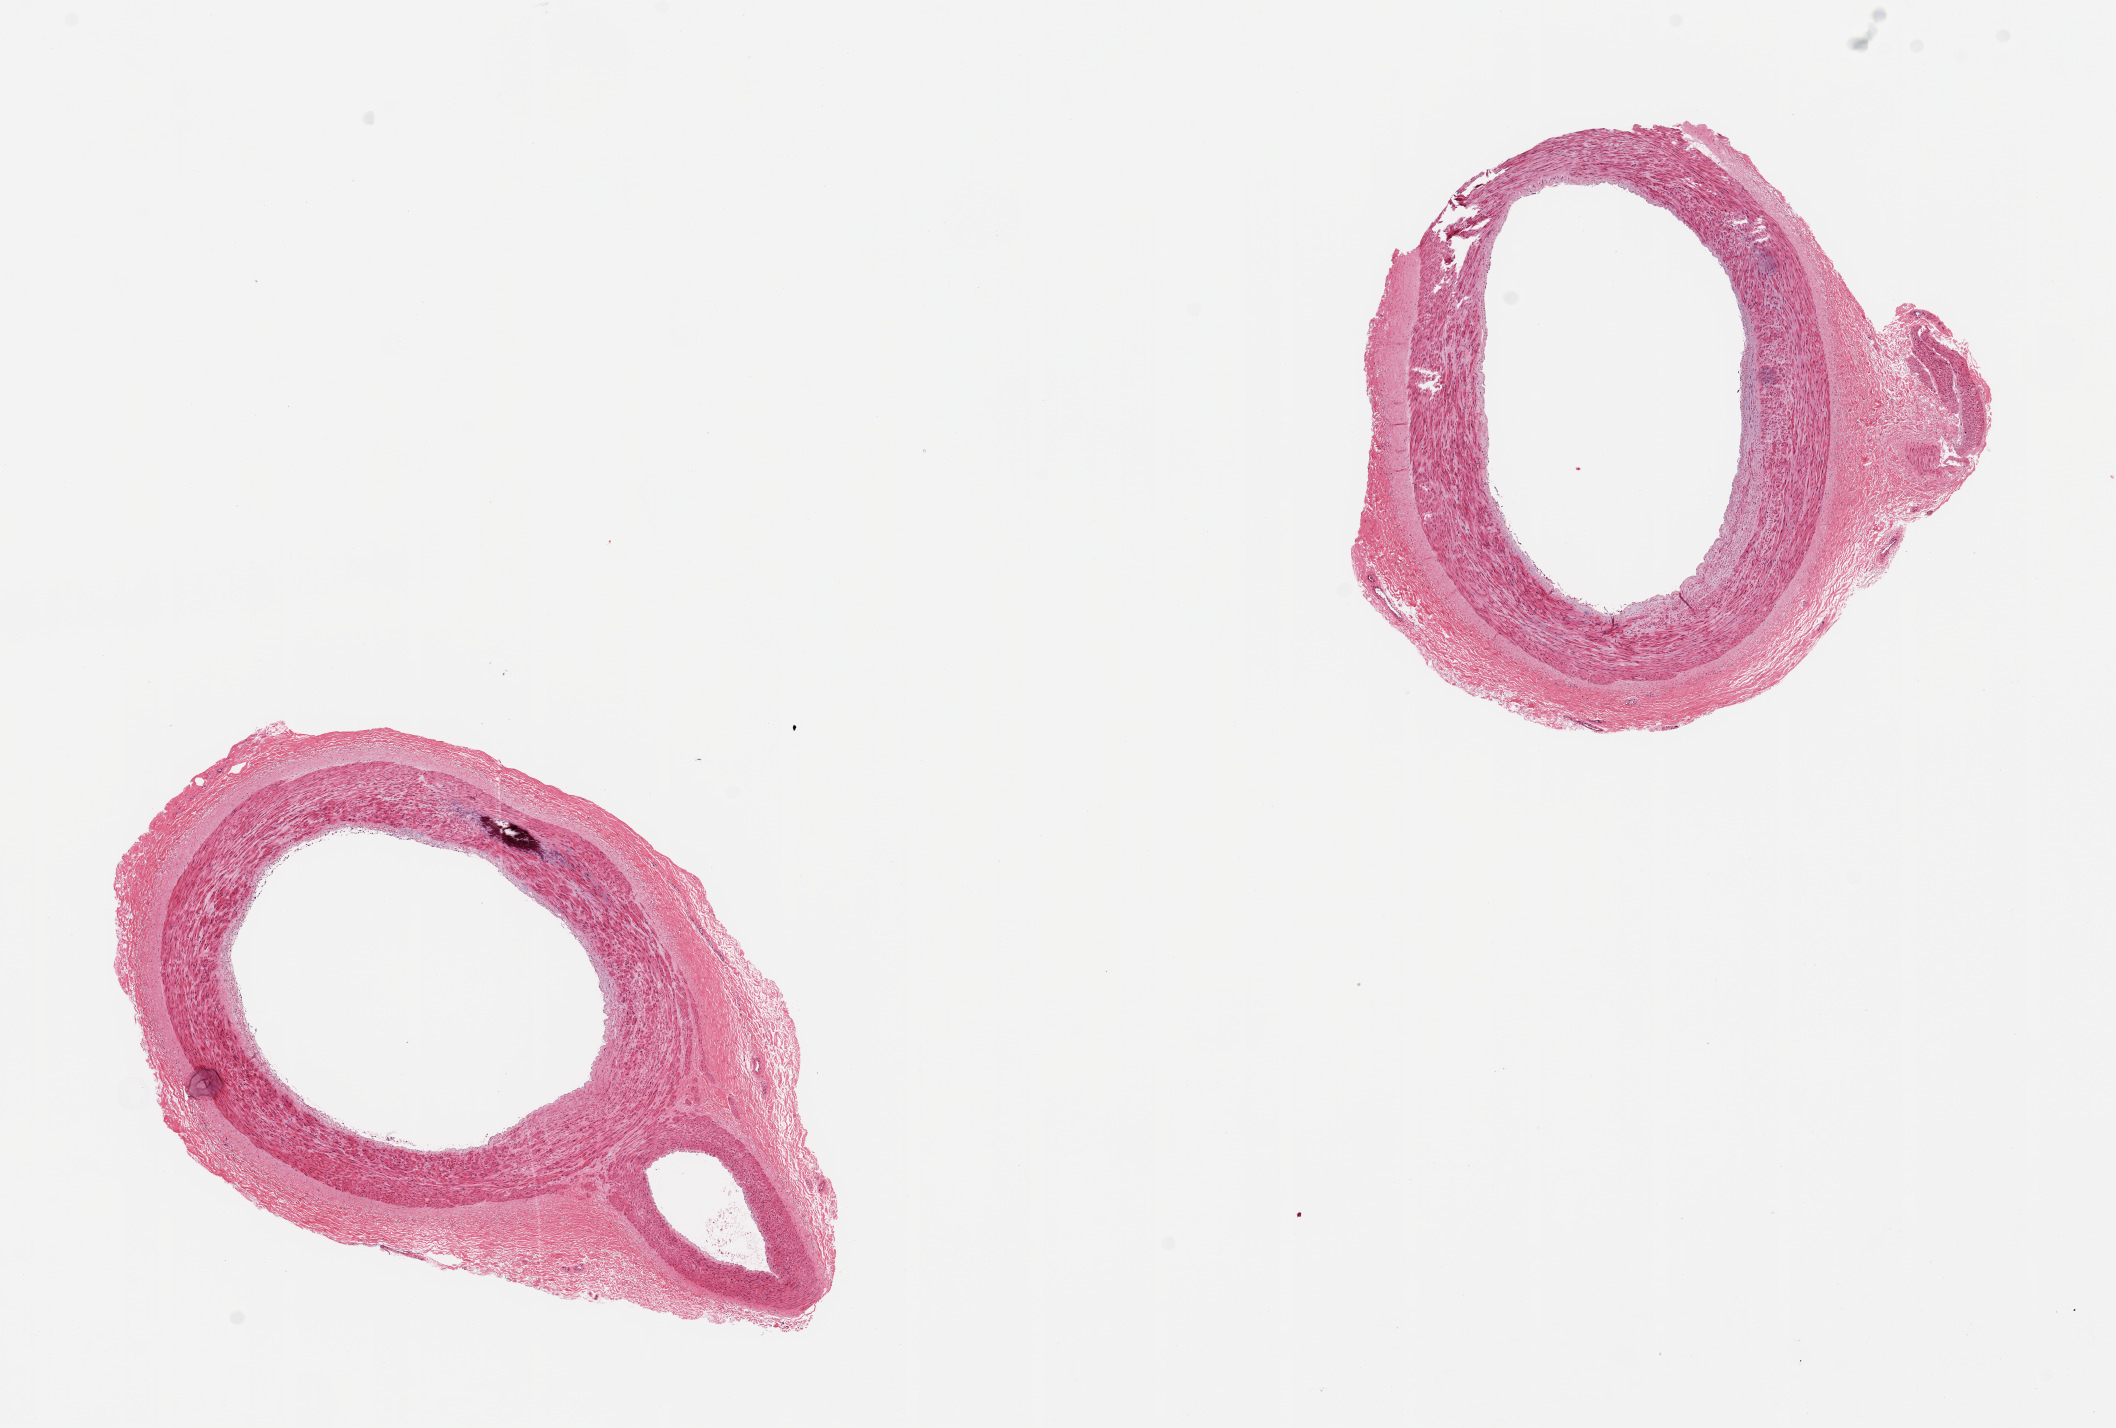
Digitized H&E-stained section, brightfield, a low-resolution overview of the entire scanned area, about 16.7 x 11.3 mm (acquisition: 20x scan), PAXgene-fixed paraffin-embedded (PFPE) section, sampled site (target tissue): tibial artery, tissue donor sample. Female donor.
Review note (as recorded): 2 pieces clean specimens; focal Monckeberg medial sclerosis.